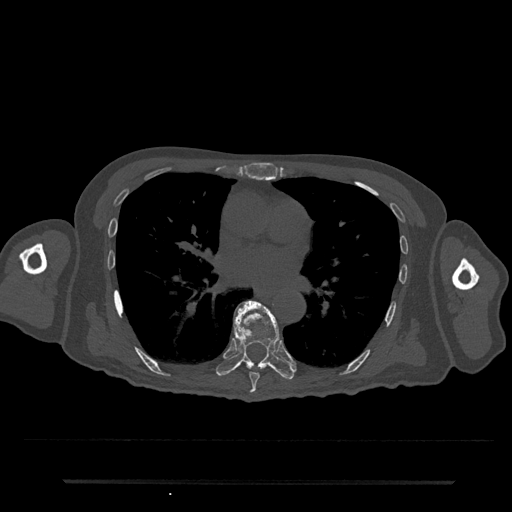
CT including the spine, one axial slice; position 444 of 797 along the scan axis; reconstruction kernel Br40s/3; 120 kVp; bone window (W 1800 / L 400 HU); 512 × 512 image matrix, field of view 427 × 427 mm. Patient: male, 74 years. Case-level facts recorded for this patient, not image findings: primary cancer: prostate.
Annotated regions visible in this slice (semi-automatic segmentation, software-assisted and operator-edited):
- T7 vertebra: bounding box [x1, y1, x2, y2] px = [249, 302, 265, 393]
- T8 vertebra: [216, 300, 295, 380]